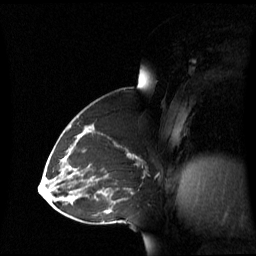
Breast MRI (dynamic contrast-enhanced), one sagittal slice; position 34 of 60 along the scan axis; dynamic contrast-enhanced series, image 2 of 3 at this slice position (ordered by acquisition); 1.5 T; TE 4.2 ms, TR 8.4 ms; 256 × 256 image matrix, field of view 270 × 270 mm. Patient: female, 43 years. Case-level facts recorded for this patient, not image findings: setting: breast cancer imaged before/during neoadjuvant chemotherapy; receptor status: triple-negative.
Annotated regions visible in this slice (semi-automatically segmented with operator editing):
- analysis volume of interest (the breast-tissue region the enhancement analysis was run in; not a lesion): bounding box [x1, y1, x2, y2] px = [69, 137, 143, 198]
- tumour enhancement mask (voxels above the 70 % enhancement threshold inside the analysis volume of interest): [127, 153, 137, 158]